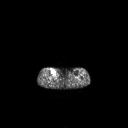
FDG PET of an extremity soft-tissue mass (from a PET/CT study), one axial slice. Slice 135 of 267 in the series (ordered by position). 128 × 128 image matrix, field of view 700 × 700 mm. Female patient, age 65 years. From the clinical record (not read from this slice): histological type: undifferentiated – high grade; grade: high; site of the primary tumour: right thigh.
Structures marked on this image (expert contour drawn on MRI and transferred to this co-registered scan by the dataset authors):
- gross tumour volume (mass): bounding box <51,69,56,74> (left, top, right, bottom; pixels)